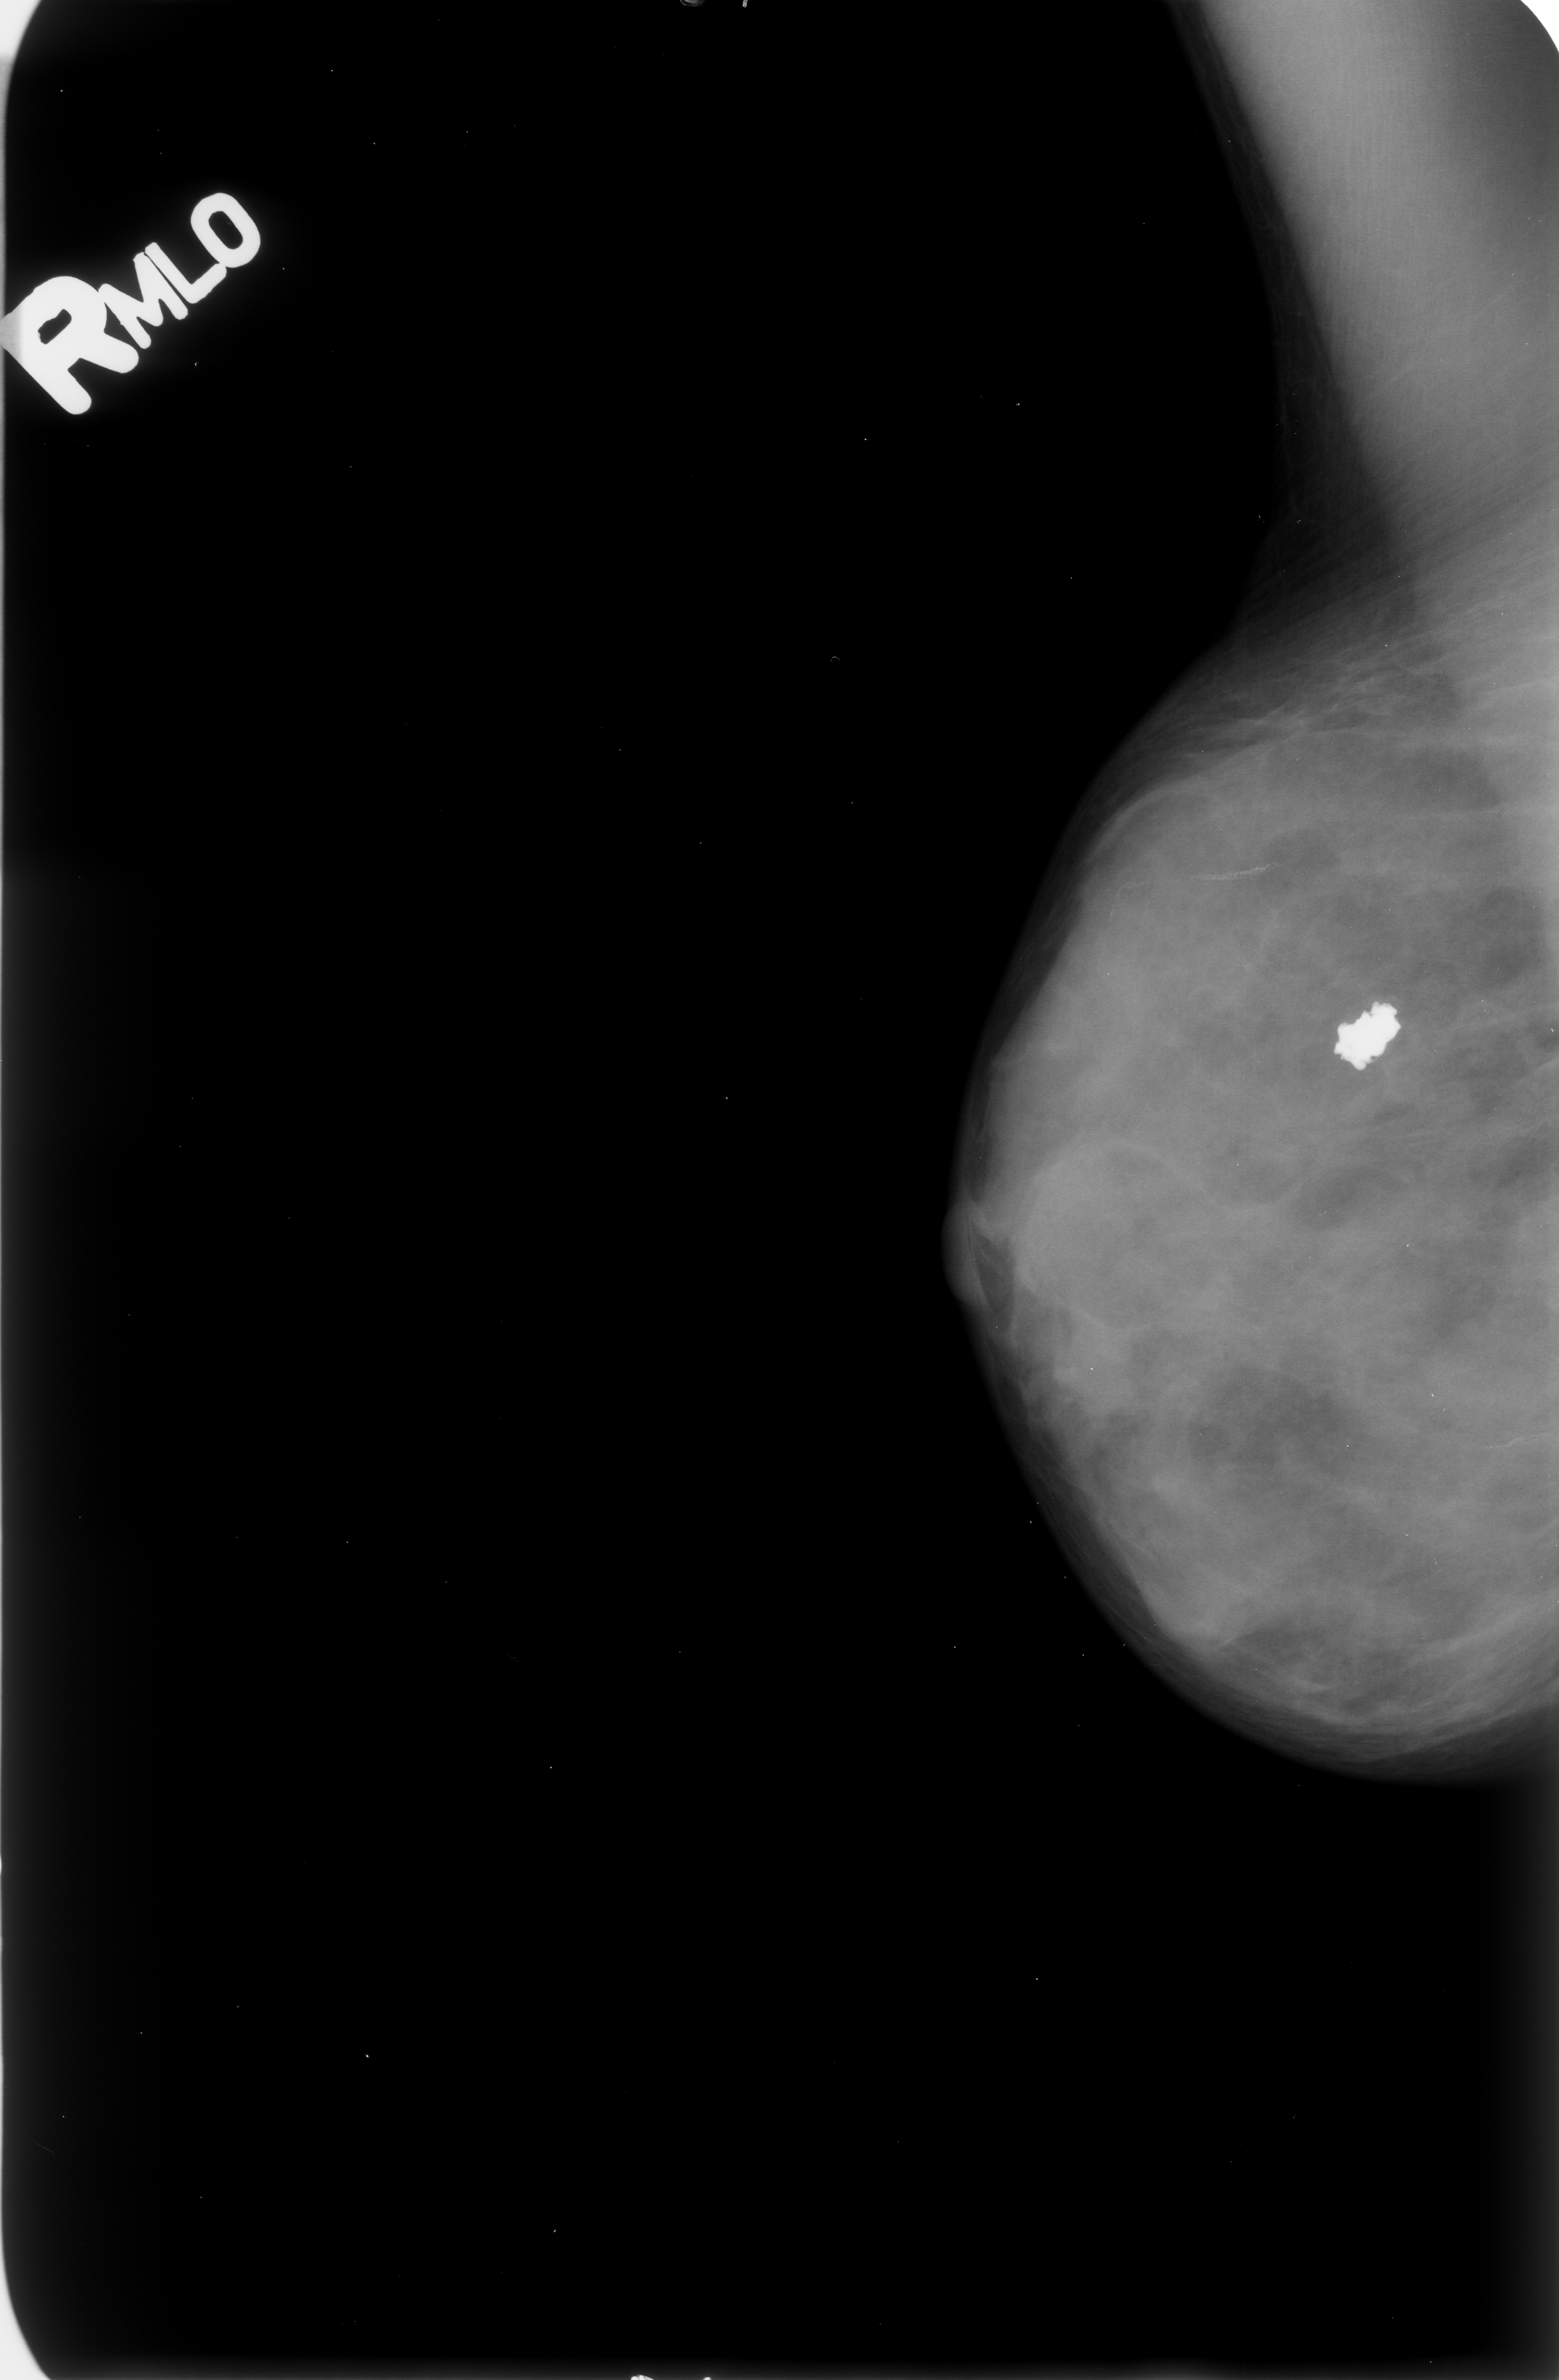
Mammogram (digitized film); right breast; mediolateral oblique (MLO) view; 1559 × 2380 image matrix.
Expert-marked regions of interest on this film, with their recorded descriptors:
- calcifications, morphology coarse; BI-RADS assessment category 2; benign; no additional work-up was recommended (outcome (as recorded, no biopsy): benign without callback): box from (x=1308, y=983) to (x=1418, y=1081) px